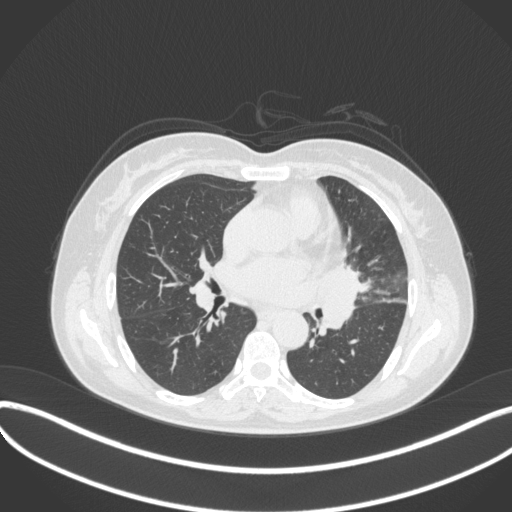
Chest CT, one axial slice; reconstruction kernel B31f; lung window (W 1500 / L -600 HU); 1 mm slice thickness; 512 × 512 image matrix, field of view 400 × 400 mm. Patient: female, 54 years. Case-level facts recorded for this patient, not image findings: clinical TNM (as recorded): T2a N1 M0; histopathological grade: G3.
Structures marked on this image (bounding box drawn by a radiologist):
- lung tumour (recorded histology: small cell carcinoma): bounding box [x1, y1, x2, y2] px = [313, 264, 371, 341]